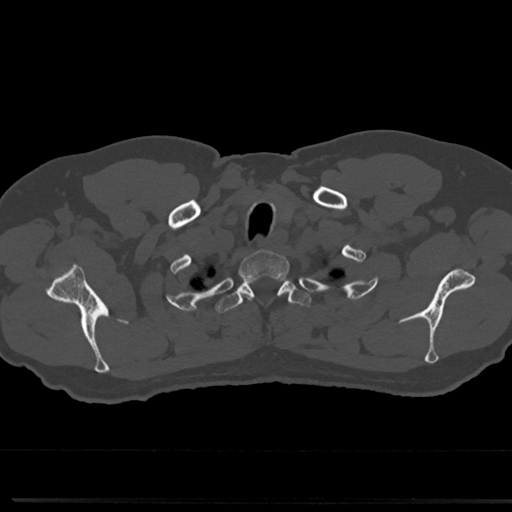
CT including the spine, one axial slice. Slice 650 of 817 in the series (ordered by position). 120 kVp. Bone window (W 1800 / L 400 HU). 0.5 mm slice thickness. 512 × 512 image matrix, field of view 355 × 355 mm. Patient: male, 61 years. Case-level facts recorded for this patient, not image findings: primary cancer: prostate.
Outlined on this slice (semi-automatically segmented with operator editing):
- T1 vertebra: bounding box (x1, y1, x2, y2) in pixels: (242, 251, 287, 269)
- T2 vertebra: (223, 274, 305, 323)